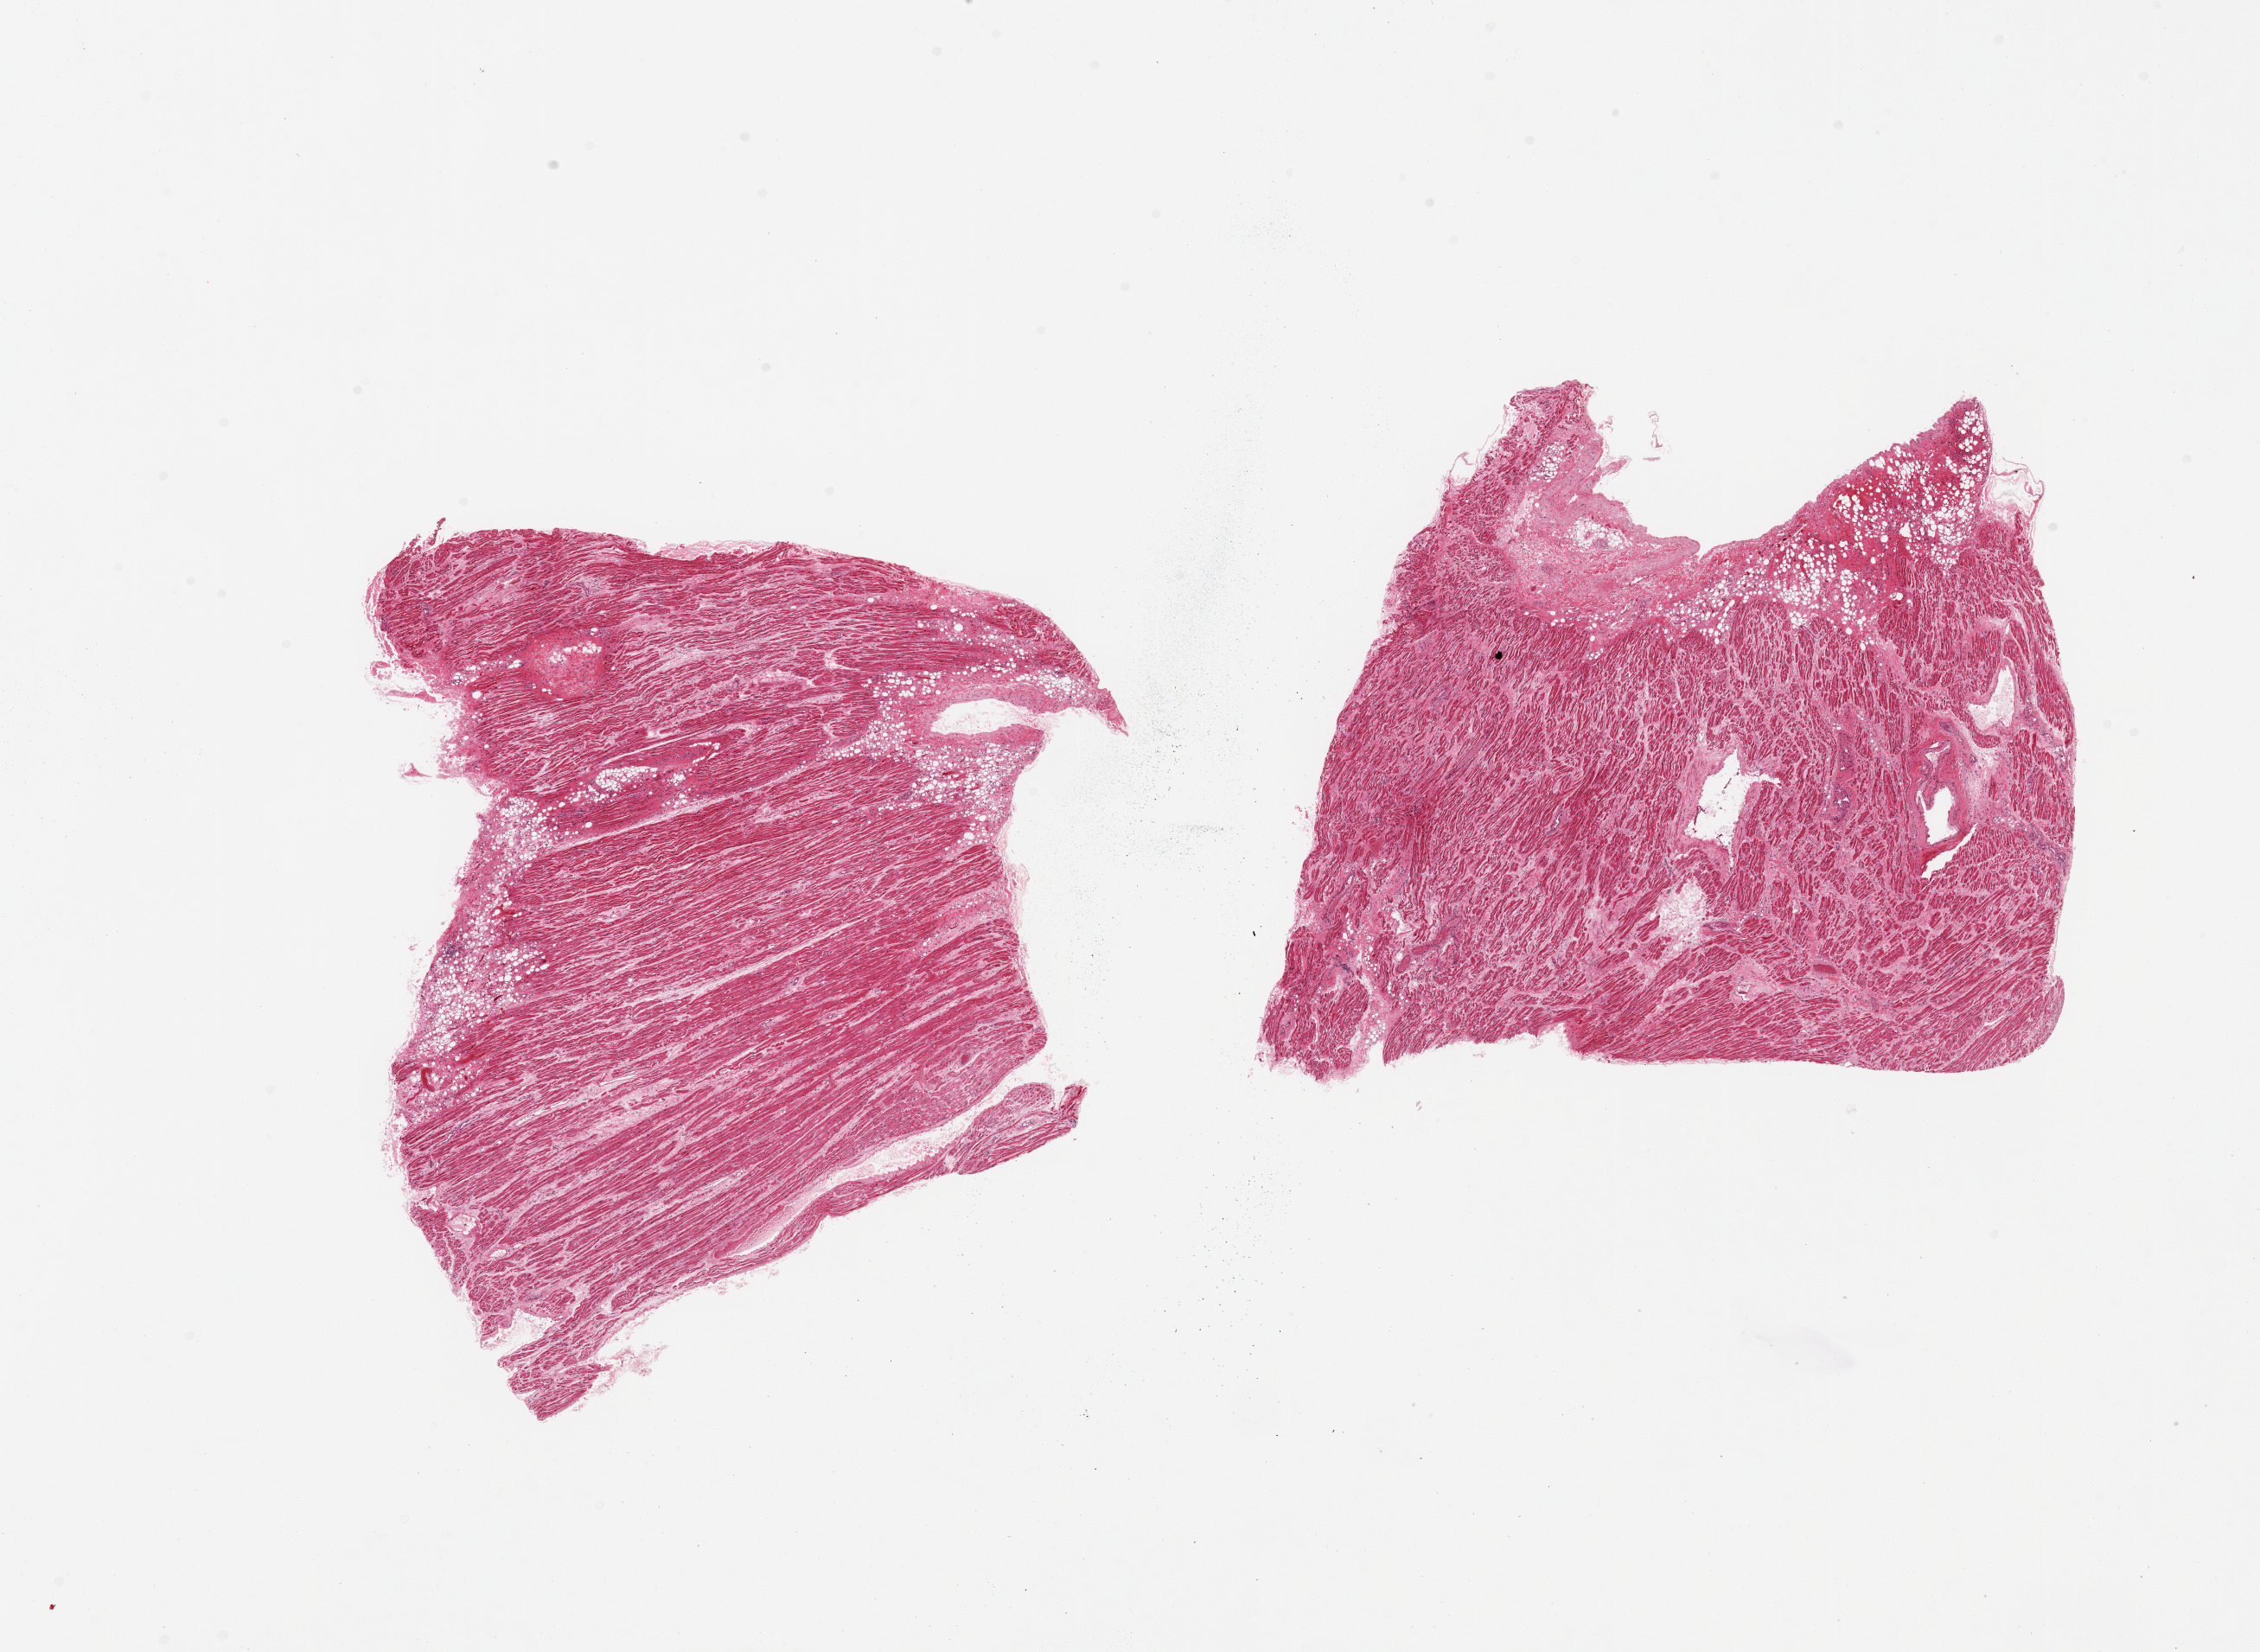
H&E whole-slide image, whole scanned area (about 20.7 x 15.1 mm) shown as a low-resolution overview; PAXgene-fixed, paraffin-embedded tissue; target tissue: auricular appendage; tissue donor sample. Donor sex: male.
Reviewer comment on this tissue sample: 2 pieces; numerous shriveled myofibers; no necrosis; 10% fibrofatty content.